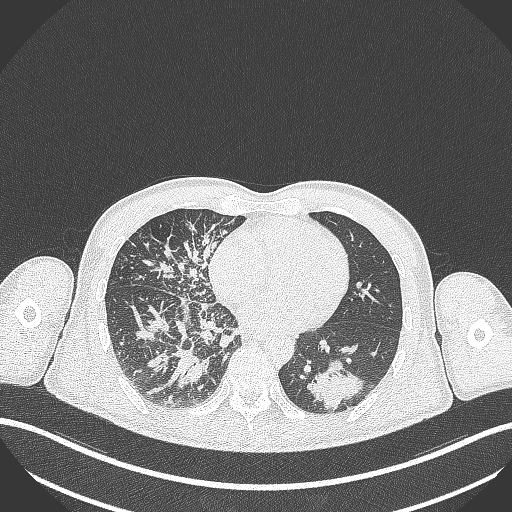
Chest CT, one axial slice. Reconstruction kernel B70f. 120 kVp. Lung window (W 1500 / L -600 HU). 512 × 512 image matrix. Patient: male, 49 years. Case-level facts recorded for this patient, not image findings: clinical TNM (as recorded): T2b N1 M0.
Structures marked on this image (bounding box drawn by a radiologist):
- lung tumour (recorded histology: adenocarcinoma): box from (x=304, y=357) to (x=366, y=412) px